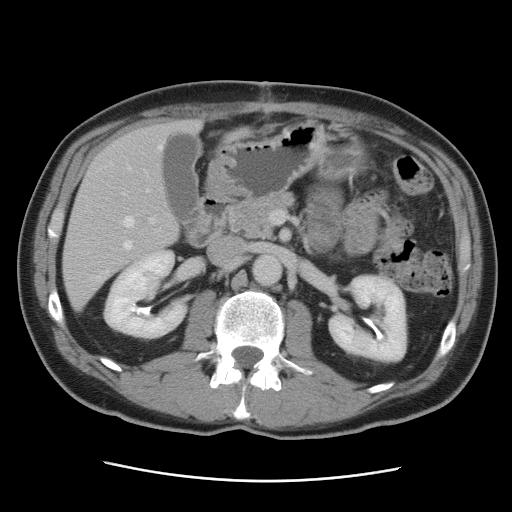
Contrast-enhanced abdominal CT, one axial slice. Position 42 of 89 along the scan axis. Intravenous contrast given. Soft-tissue window (W 400 / L 40 HU). 5 mm slice thickness. 512 × 512 image matrix, field of view 366 × 366 mm. Male patient, age 59 years. Case-level facts recorded for this patient, not image findings: diagnosis: colorectal cancer liver metastases, imaged before liver resection; multiple liver metastases: yes; largest metastasis: 0.6 cm; disease in both lobes: yes.
Structures marked on this image (outlined manually by an expert reader):
- hepatic veins: bounding box <95,145,163,282> (left, top, right, bottom; pixels)
- liver: <64,119,246,311>
- planned liver remnant (the part of the liver to remain after resection): <73,120,201,245>
- portal vein (with intrahepatic branches): <123,189,155,223>
- liver metastasis: <238,133,244,138>